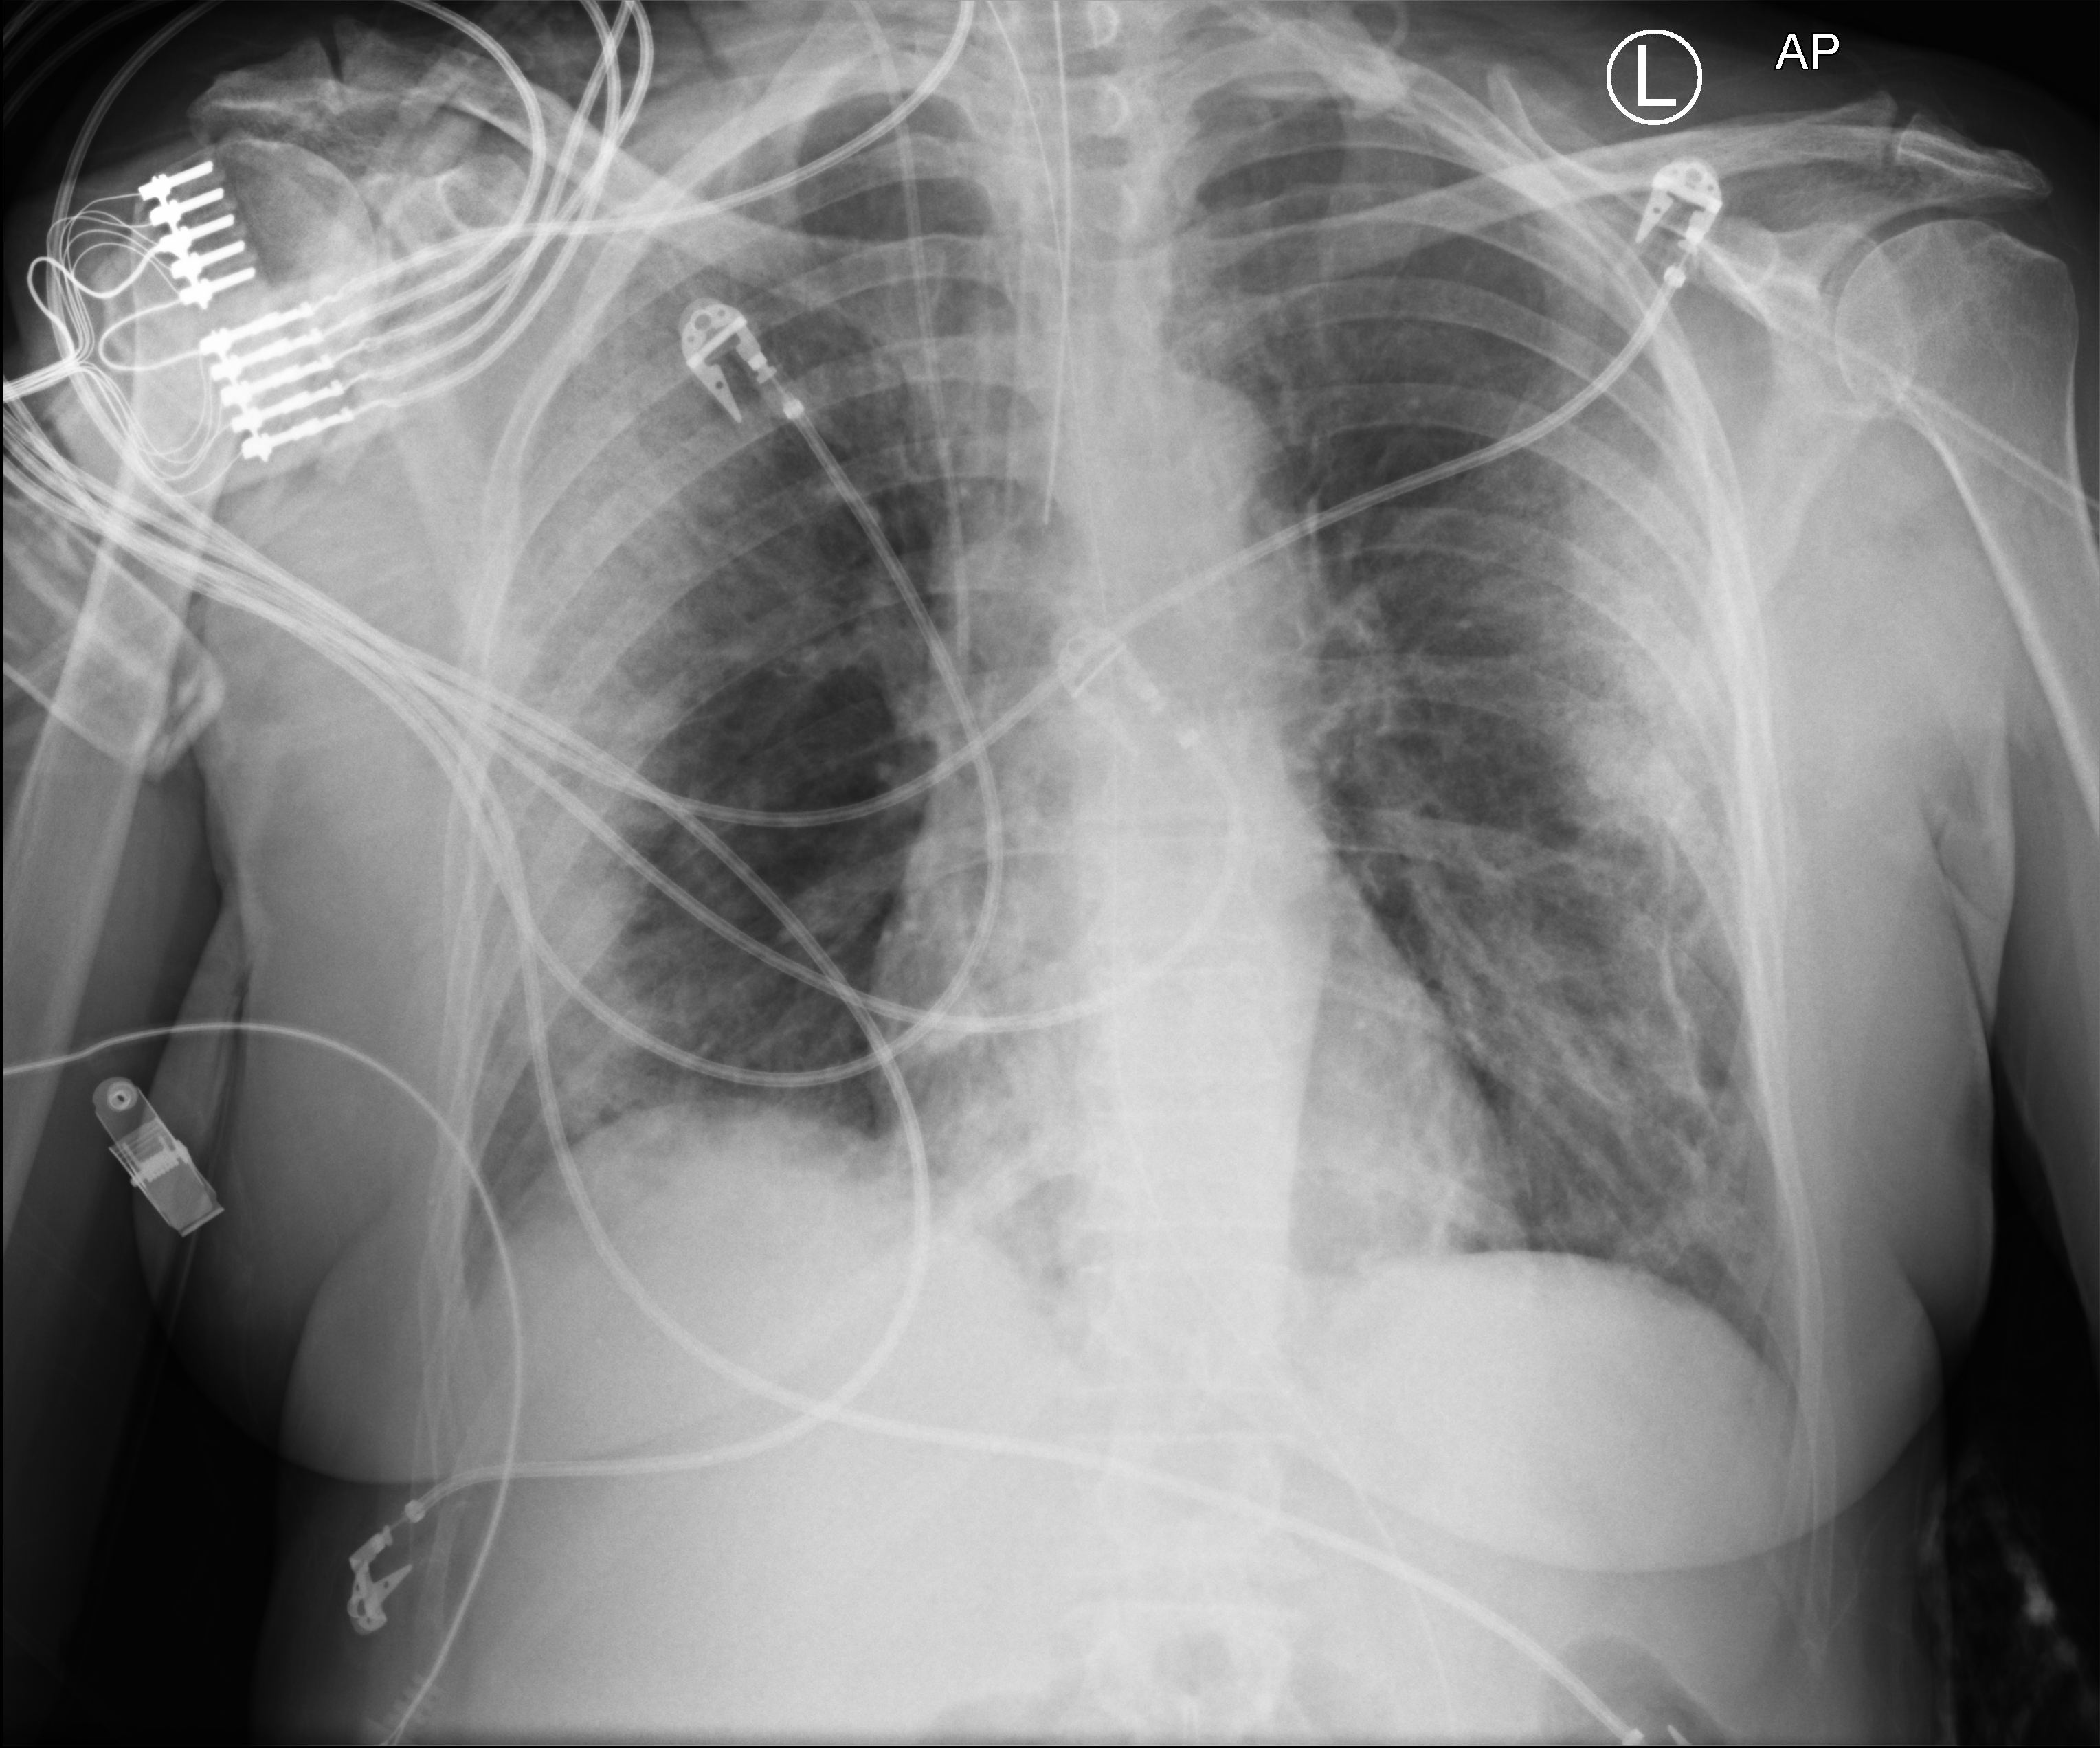
Portable chest radiograph; anteroposterior (AP) projection. Patient hospitalised with COVID-19; female, aged 60–74 years.
From the hospital-stay record, not from the radiograph (when in the stay this image was taken is not recorded): admitted to intensive care during this hospital stay: yes; chronic kidney disease (admission record): no.